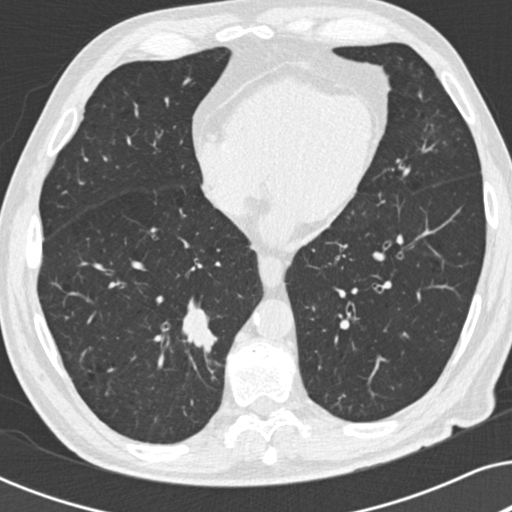
Low-dose screening chest CT, one axial slice. Slice 84 of 191 in the series (ordered by position). Reconstruction kernel B30f. 120 kVp. Lung window (W 1500 / L -600 HU). 2 mm slice thickness. 512 × 512 image matrix, field of view 330 × 330 mm.
Outlined on this slice (outlined manually by an expert reader):
- lesion 1 (tumor, lower lobe of right lung): bounding box <182,307,217,344> (left, top, right, bottom; pixels)